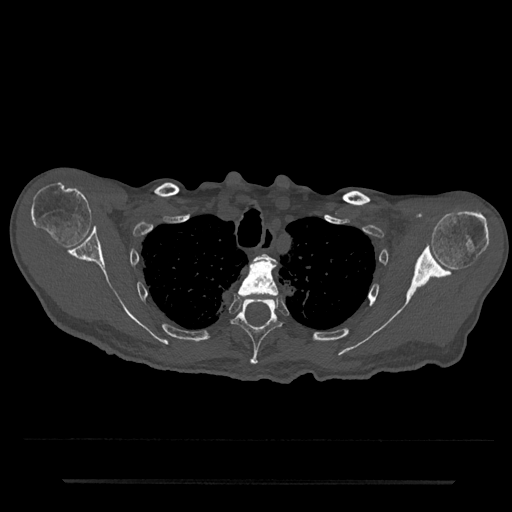
CT including the spine, one axial slice. Reconstruction kernel Br40s/3. 120 kVp. Bone window (W 1800 / L 400 HU). 512 × 512 image matrix, field of view 427 × 427 mm. Patient: male, 74 years. From the clinical record (not read from this slice): primary cancer: prostate.
Outlined on this slice (semi-automatically segmented with operator editing):
- T2 vertebra: bounding box <256,253,273,261> (left, top, right, bottom; pixels)
- T3 vertebra: <238,259,279,296>
- T4 vertebra: <233,299,282,365>